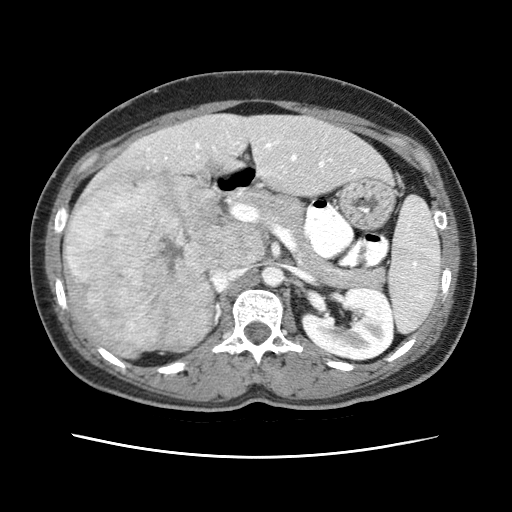
Contrast-enhanced abdominal CT (liver protocol), one axial slice; slice 26 of 79 in the series (ordered by position); soft-tissue window (W 400 / L 40 HU); 2.5 mm slice thickness; 512 × 512 image matrix, field of view 340 × 340 mm. From the clinical record (not read from this slice): diagnosis: hepatocellular carcinoma (patient treated with transarterial chemoembolisation; whether this scan precedes or follows treatment is not stated here); TNM stage (as recorded): Stage-I; Child-Pugh class: A; tumour differentiation: moderately differentiated; tumour nodularity: uninodular.
Annotated regions visible in this slice (semi-automatic segmentation, software-assisted and operator-edited):
- abdominal aorta: box from (x=262, y=267) to (x=283, y=285) px
- liver parenchyma outside the tumour (the mass and vessels are separate outlines, so this box may not span the whole liver): (x=64, y=114)–(x=390, y=356)
- mass: (x=65, y=166)–(x=223, y=357)
- liver vessels: (x=147, y=141)–(x=355, y=173)